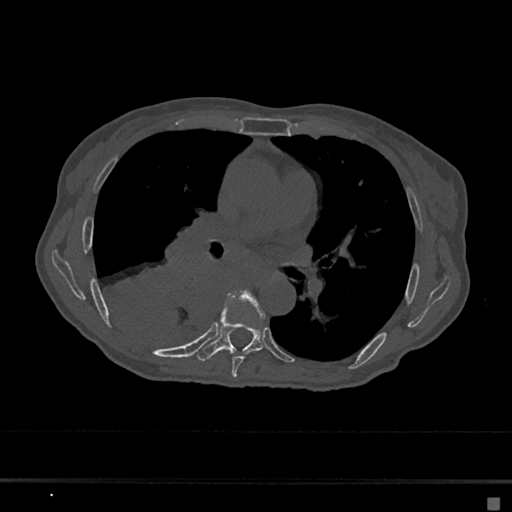
CT including the spine, one axial slice; slice 393 of 797 in the series (ordered by position); bone window (W 1800 / L 400 HU); 0.5 mm slice thickness; 512 × 512 image matrix, field of view 360 × 360 mm. Female patient, age 68 years. From the clinical record (not read from this slice): primary cancer: renal.
Annotated regions visible in this slice (semi-automatic segmentation, software-assisted and operator-edited):
- T6 vertebra: box from (x=231, y=291) to (x=265, y=378) px
- T7 vertebra: (x=197, y=295)–(x=264, y=361)